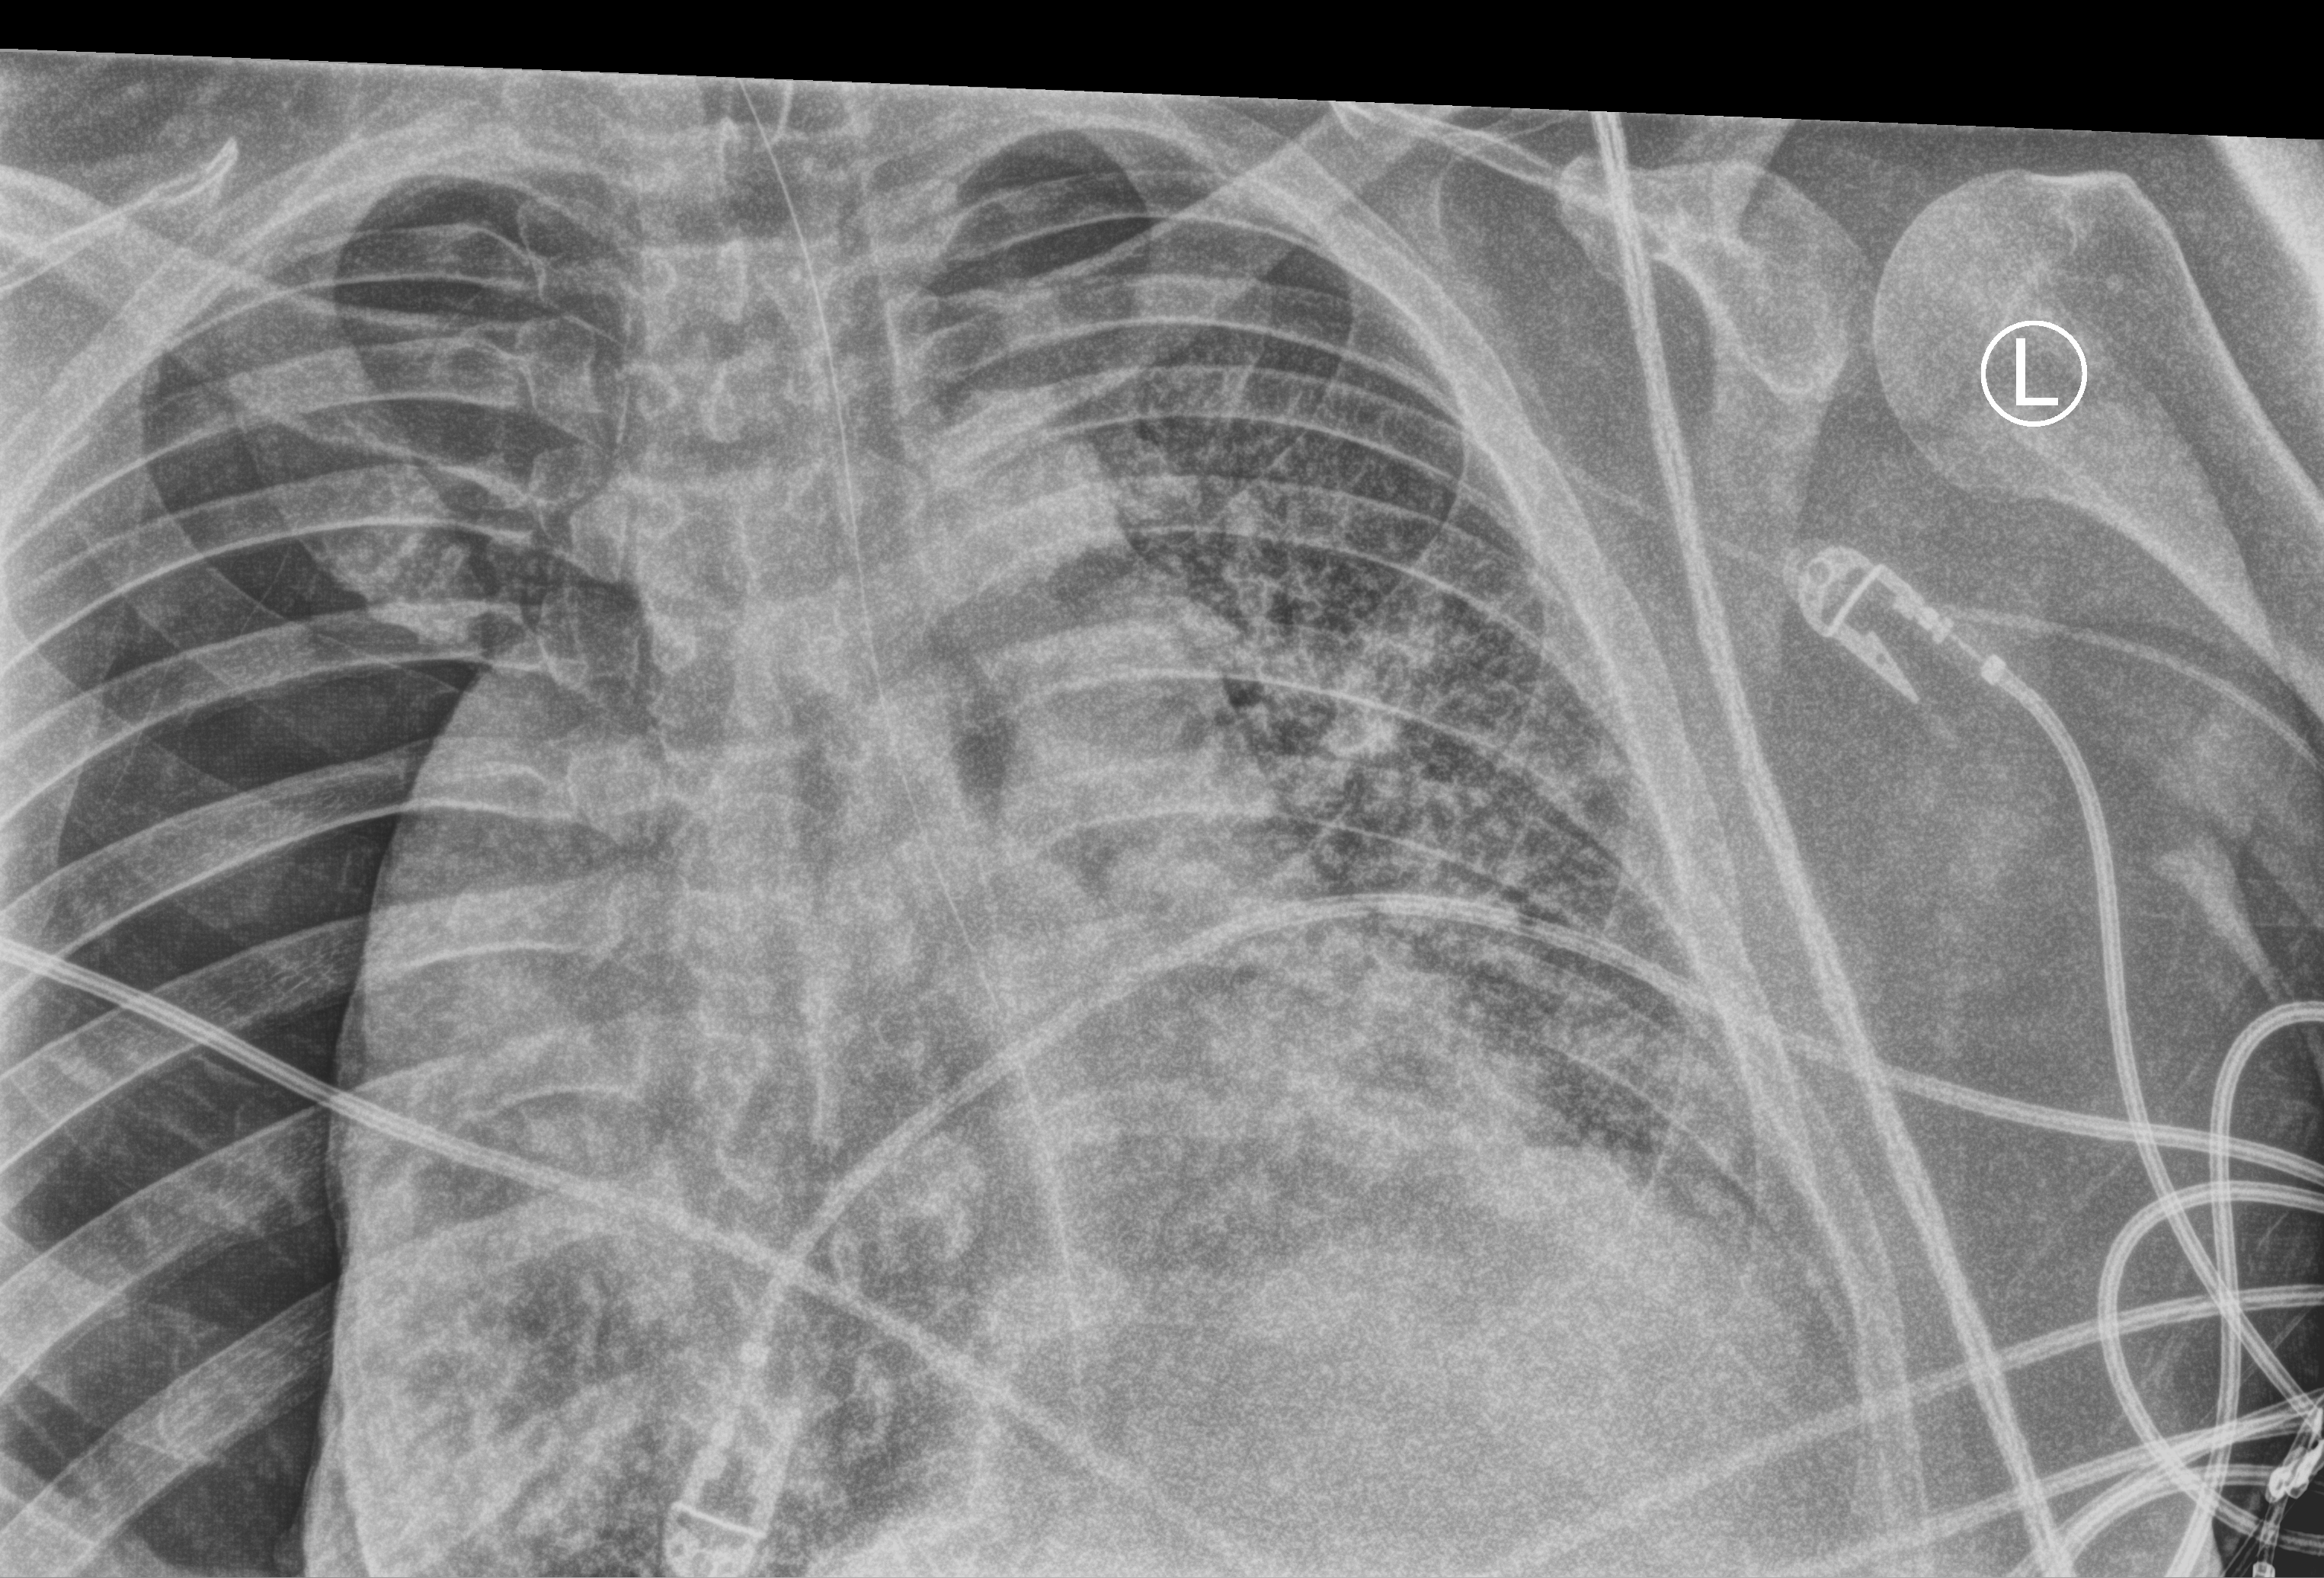
Portable chest radiograph. Patient hospitalised with COVID-19, aged 18–59 years.
Hospital-stay facts (about this admission, not read from this image; timing relative to this image not recorded): mechanically ventilated during this hospital stay: yes.